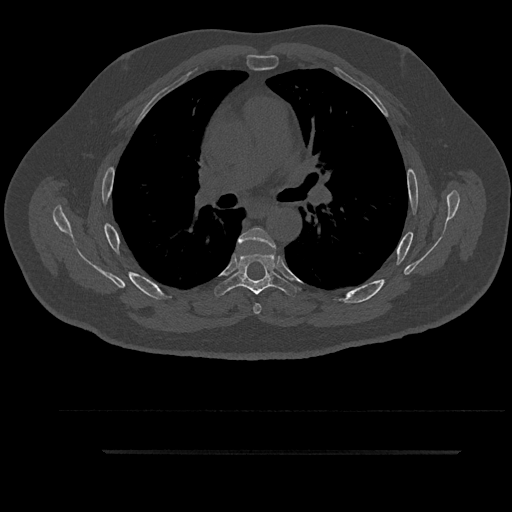
CT including the spine, one axial slice. Position 593 of 797 along the scan axis. Reconstruction kernel Br40s/3. Bone window (W 1800 / L 400 HU). 0.5 mm slice thickness. 512 × 512 image matrix. Male patient, age 63 years. From the clinical record (not read from this slice): primary cancer: renal.
Outlined on this slice (semi-automatically segmented with operator editing):
- T5 vertebra: bounding box (x1, y1, x2, y2) in pixels: (238, 227, 276, 314)
- T6 vertebra: (216, 248, 298, 295)